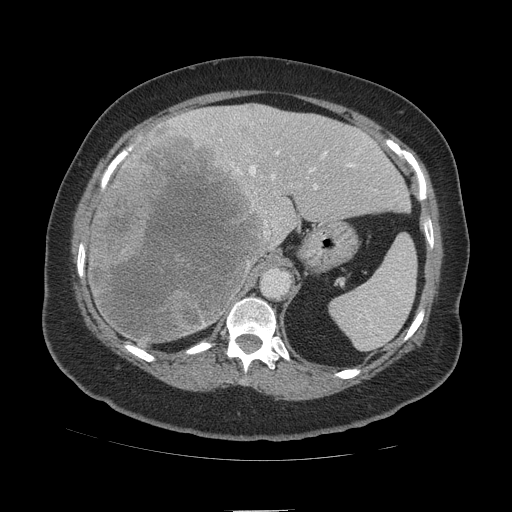
Contrast-enhanced abdominal CT (liver protocol), one axial slice. Slice 74 of 109 in the series (ordered by position). Soft-tissue window (W 400 / L 40 HU). 512 × 512 image matrix. Case-level facts recorded for this patient, not image findings: diagnosis: hepatocellular carcinoma (patient treated with transarterial chemoembolisation; whether this scan precedes or follows treatment is not stated here); TNM stage (as recorded): Stage-IVB; Child-Pugh class: A; tumour differentiation: poorly differentiated; tumour nodularity: multinodular.
Annotated regions visible in this slice (semi-automatic segmentation, software-assisted and operator-edited):
- liver parenchyma outside the tumour (the mass and vessels are separate outlines, so this box may not span the whole liver): bounding box <88,104,408,340> (left, top, right, bottom; pixels)
- mass: <89,130,276,350>
- liver vessels: <169,118,355,190>